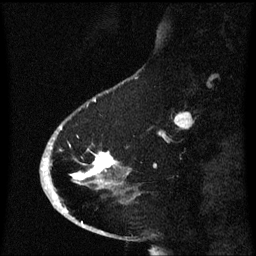
Breast MRI (dynamic contrast-enhanced), one sagittal slice; slice 17 of 60 in the series (ordered by position); dynamic contrast-enhanced series, image 2 of 3 at this slice position (ordered by acquisition); 1.5 T; TE 4.2 ms, TR 8.4 ms; 256 × 256 image matrix, field of view 200 × 200 mm. Female patient, age 53 years. From the clinical record (not read from this slice): setting: breast cancer imaged before/during neoadjuvant chemotherapy; receptor status: HR-positive, HER2-negative.
Outlined on this slice (semi-automatically segmented with operator editing):
- analysis volume of interest (the breast-tissue region the enhancement analysis was run in; not a lesion): box from (x=49, y=118) to (x=130, y=201) px
- tumour enhancement mask (voxels above the 70 % enhancement threshold inside the analysis volume of interest): (x=75, y=154)–(x=116, y=181)